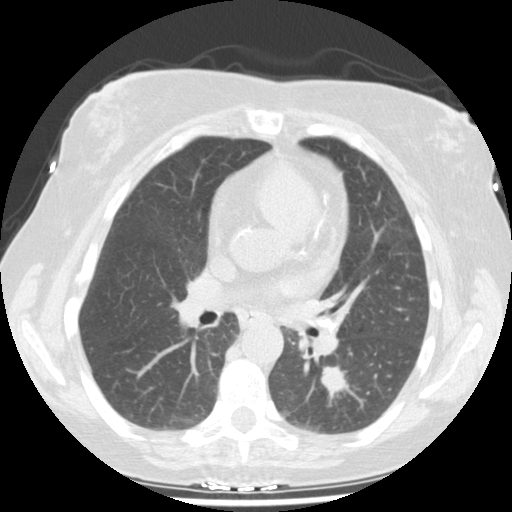
Low-dose screening chest CT, one axial slice. Position 94 of 159 along the scan axis. 120 kVp. Lung window (W 1500 / L -600 HU). 2.5 mm slice thickness. 512 × 512 image matrix, field of view 326 × 326 mm.
Structures marked on this image (outlined manually by an expert reader):
- lesion 1 (tumor, lower lobe of left lung): box from (x=320, y=365) to (x=350, y=404) px